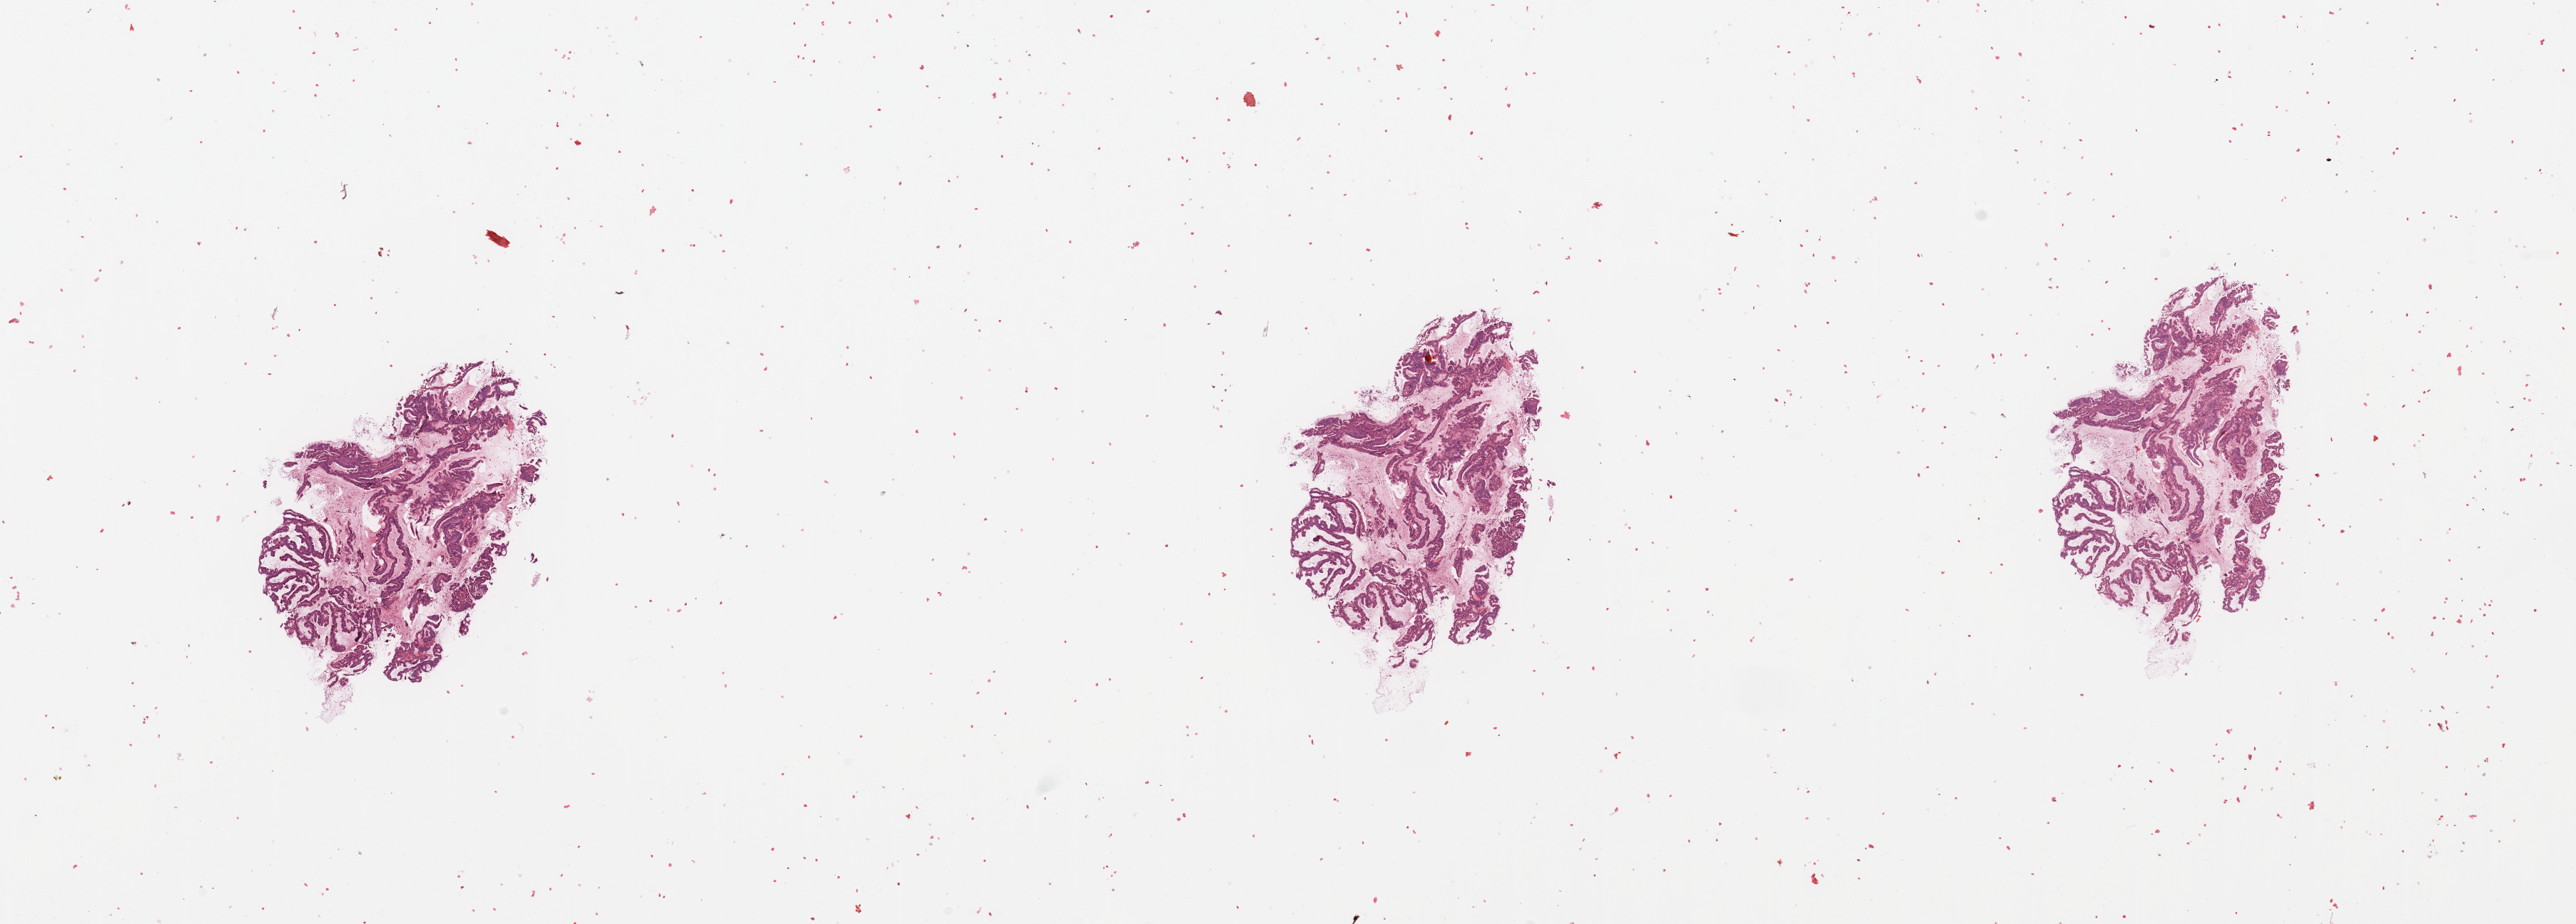
Hematoxylin and eosin (H&E) stained whole-slide image — low-resolution overview of the scanned area, about 28.5 x 10.2 mm. Tumour tissue sample, sampled site: uterus. Female, 66 y/o. Slide review estimates, as recorded: tumour nuclei 90%, necrosis 2%.
Histologic diagnosis: Endometrioid adenocarcinoma, NOS.